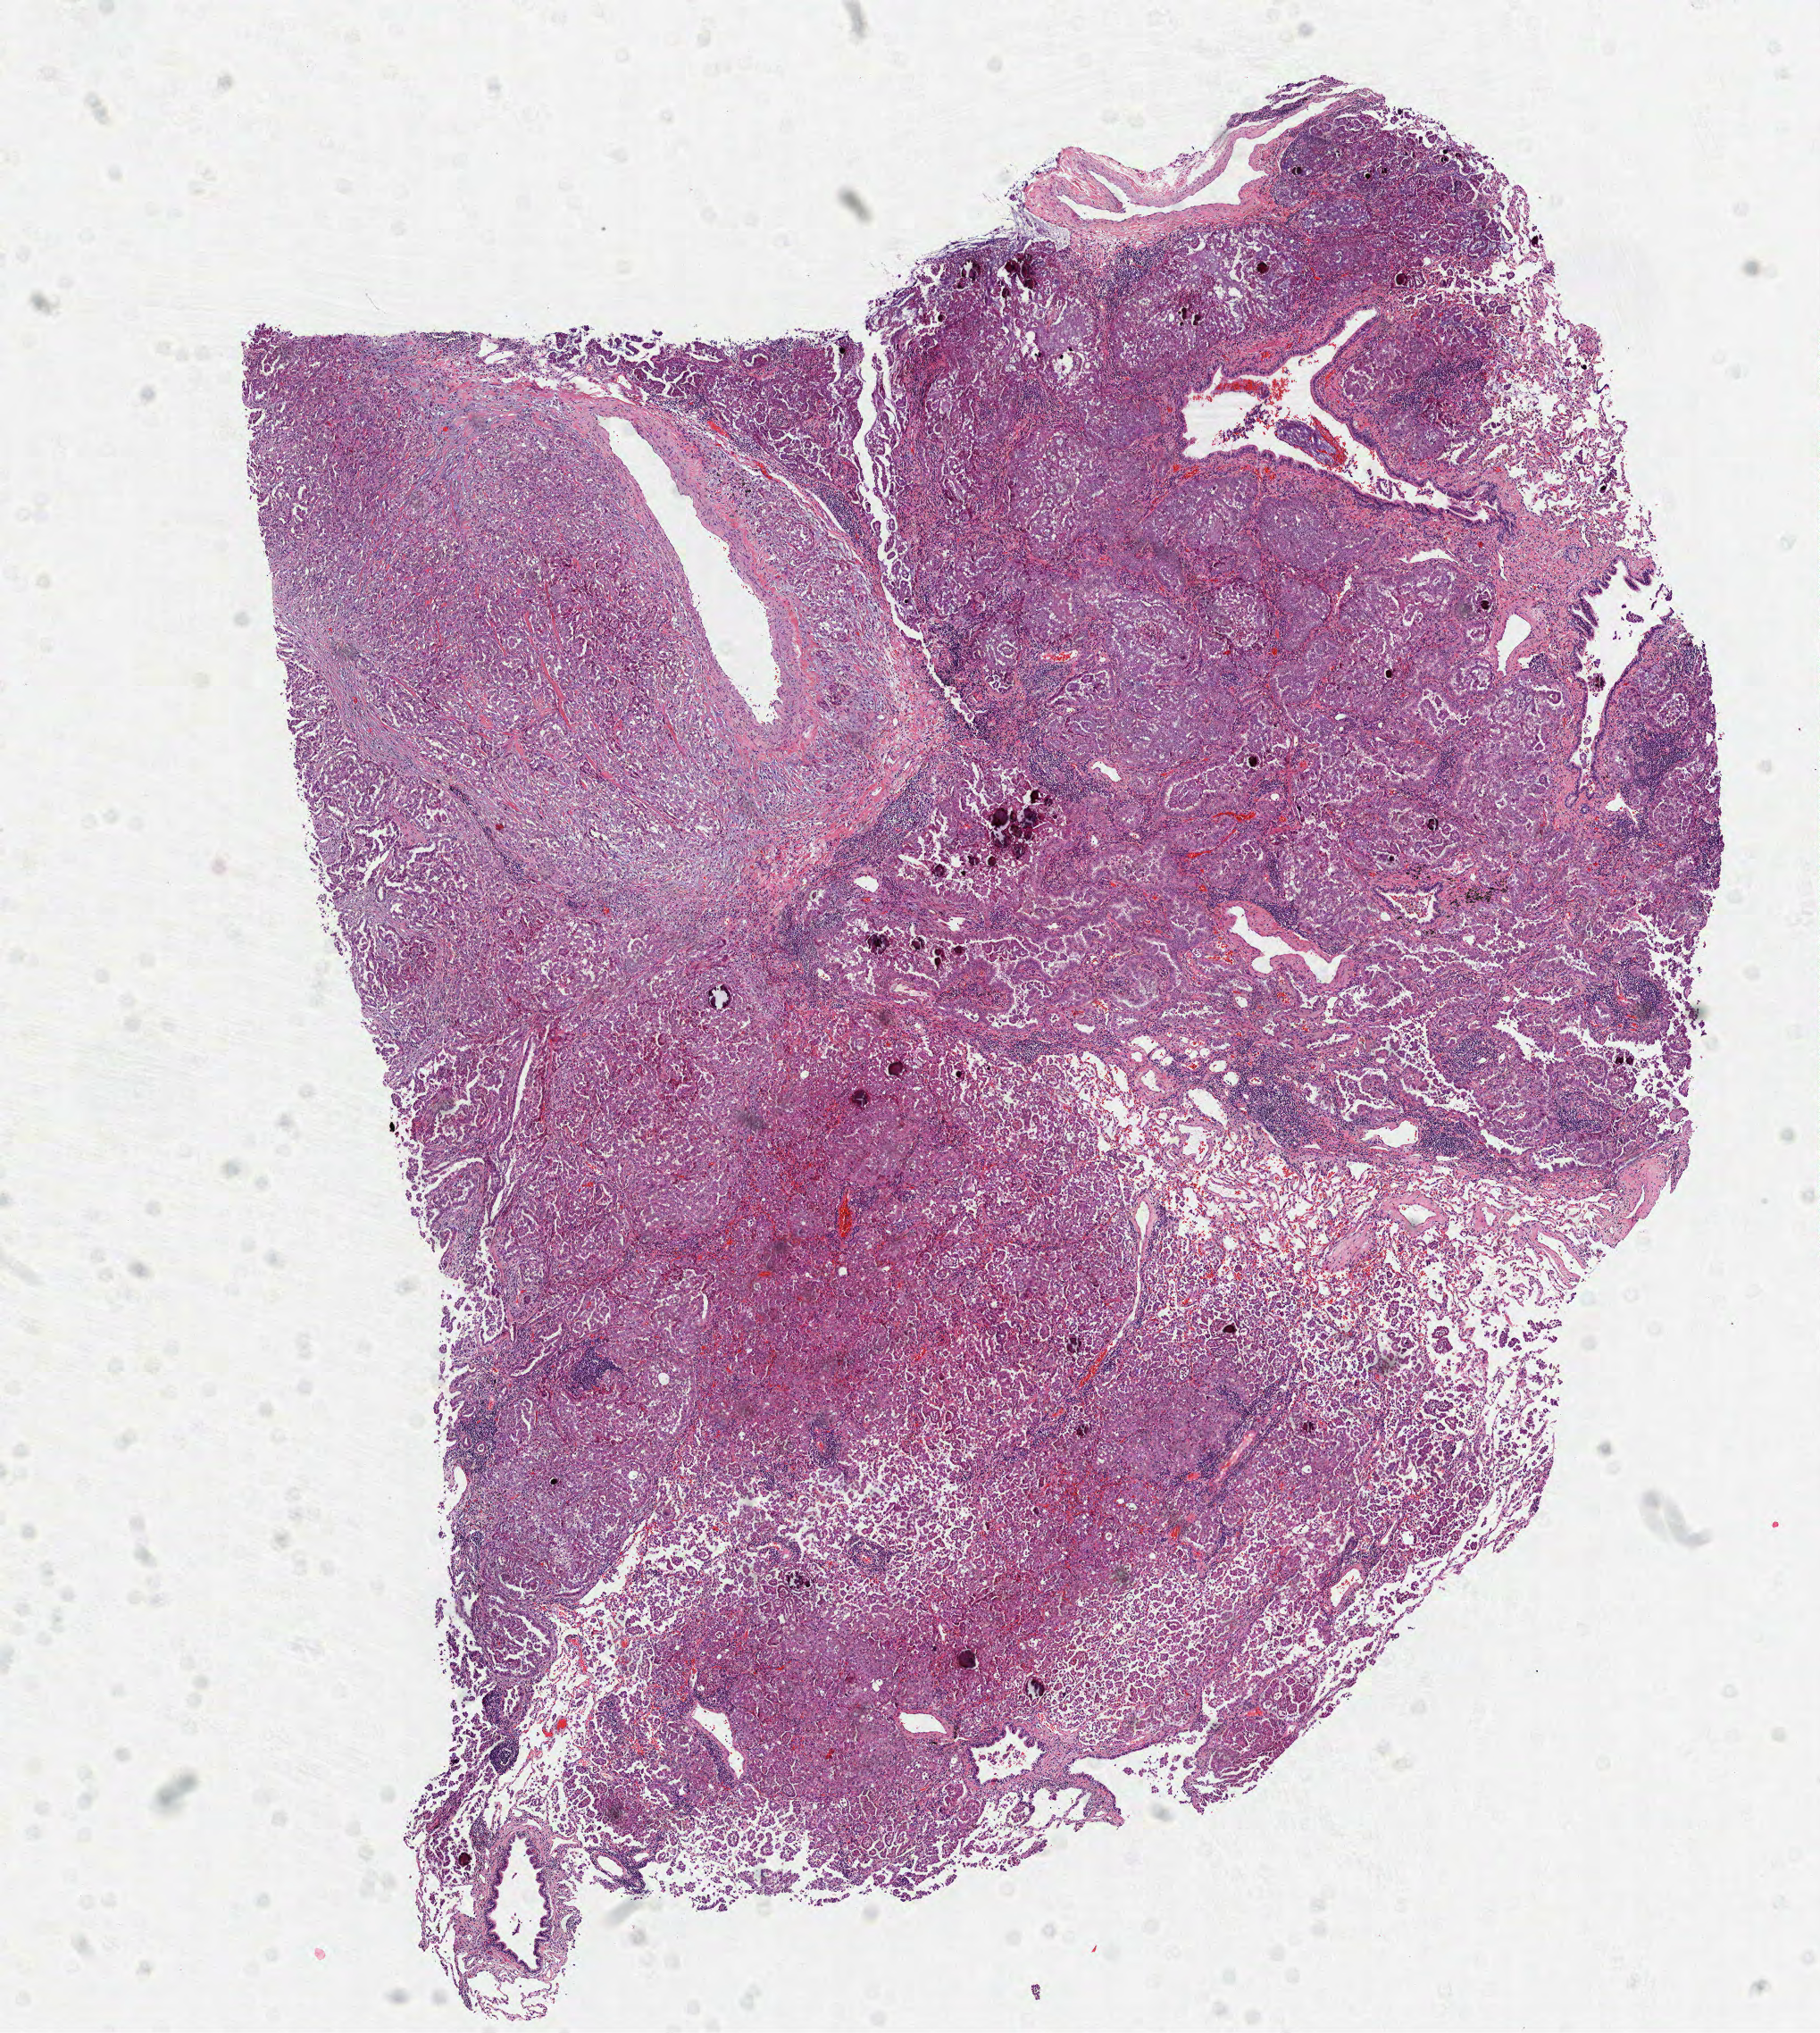
Hematoxylin and eosin (H&E) stained whole-slide image — whole scanned area (about 8.2 x 9.2 mm) shown as a low-resolution overview. Frozen section. Primary tumour sample from the lung. Patient: female, age at initial diagnosis 57 years. Composition of this section per pathologist review: tumour cells 70%, tumour nuclei 70%, normal cells 10%, stromal cells 20%, necrosis 0%.
• histologic diagnosis: Adenocarcinoma, NOS (middle lobe, lung)
• AJCC pathologic stage: IA